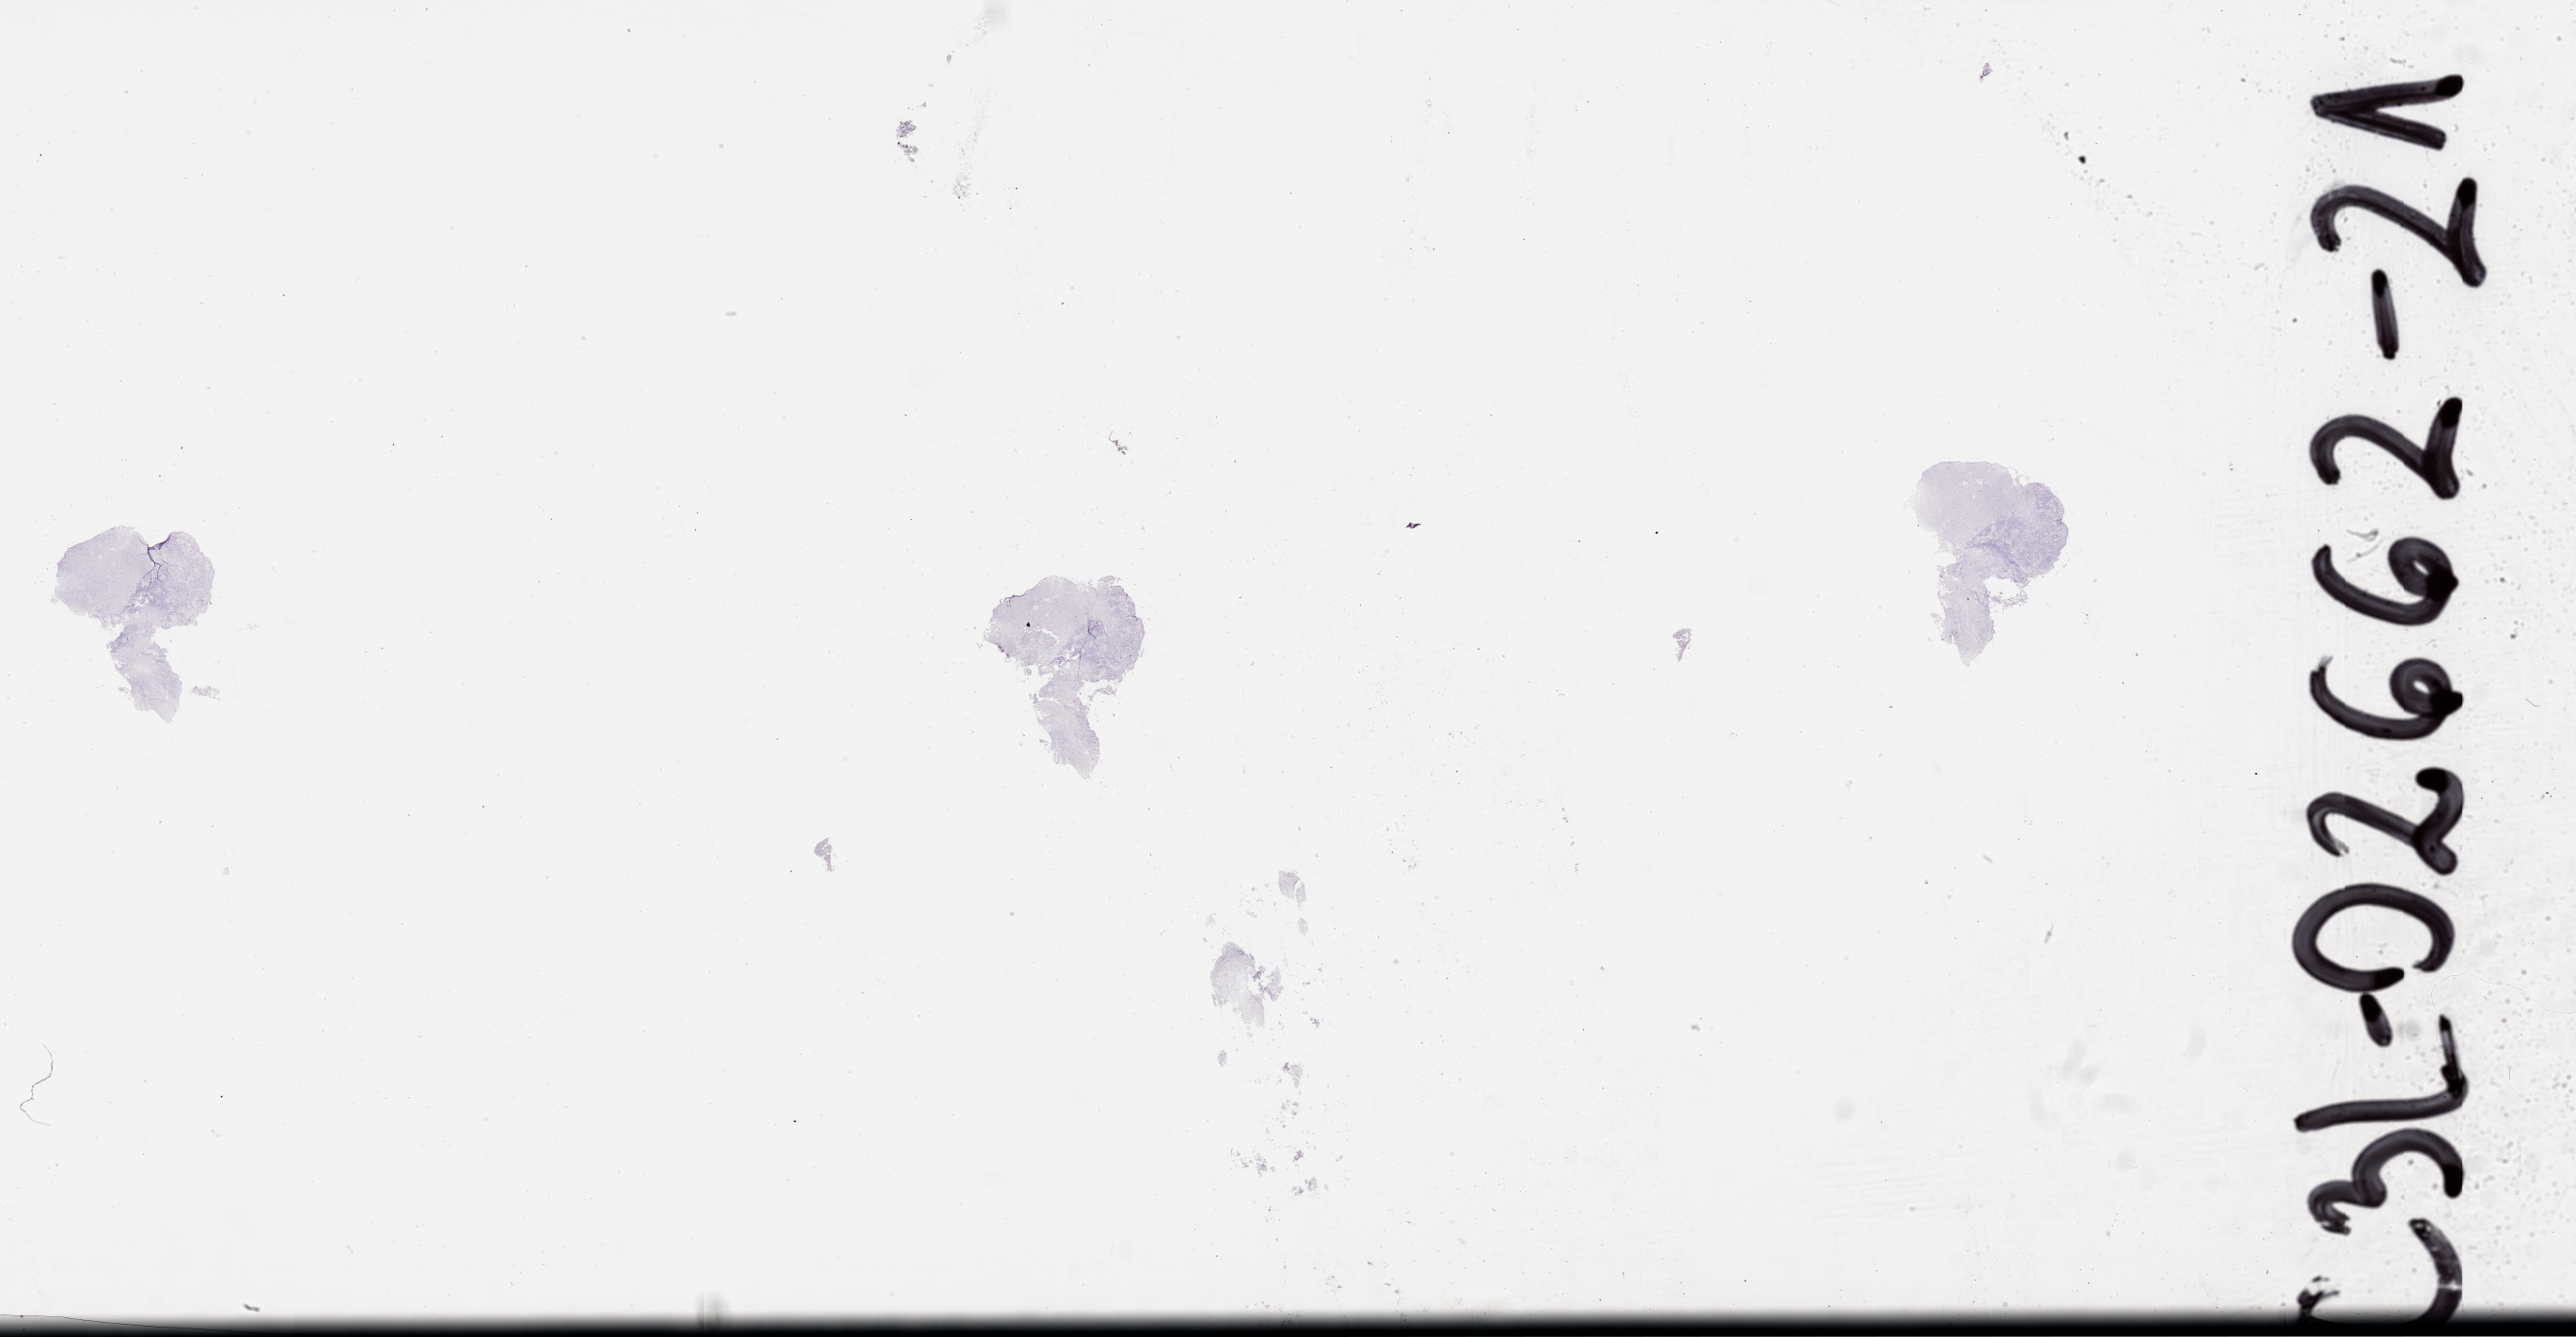
Whole-slide histology image, Hematoxylin and eosin (H&E) stained, a low-resolution overview of the entire scanned area, about 44.1 x 22.9 mm (slide scanned at 20x). Brain, tumour tissue. 65-year-old male patient.
- histologic diagnosis: Glioblastoma
- primary tumour site (as recorded): parietal lobe